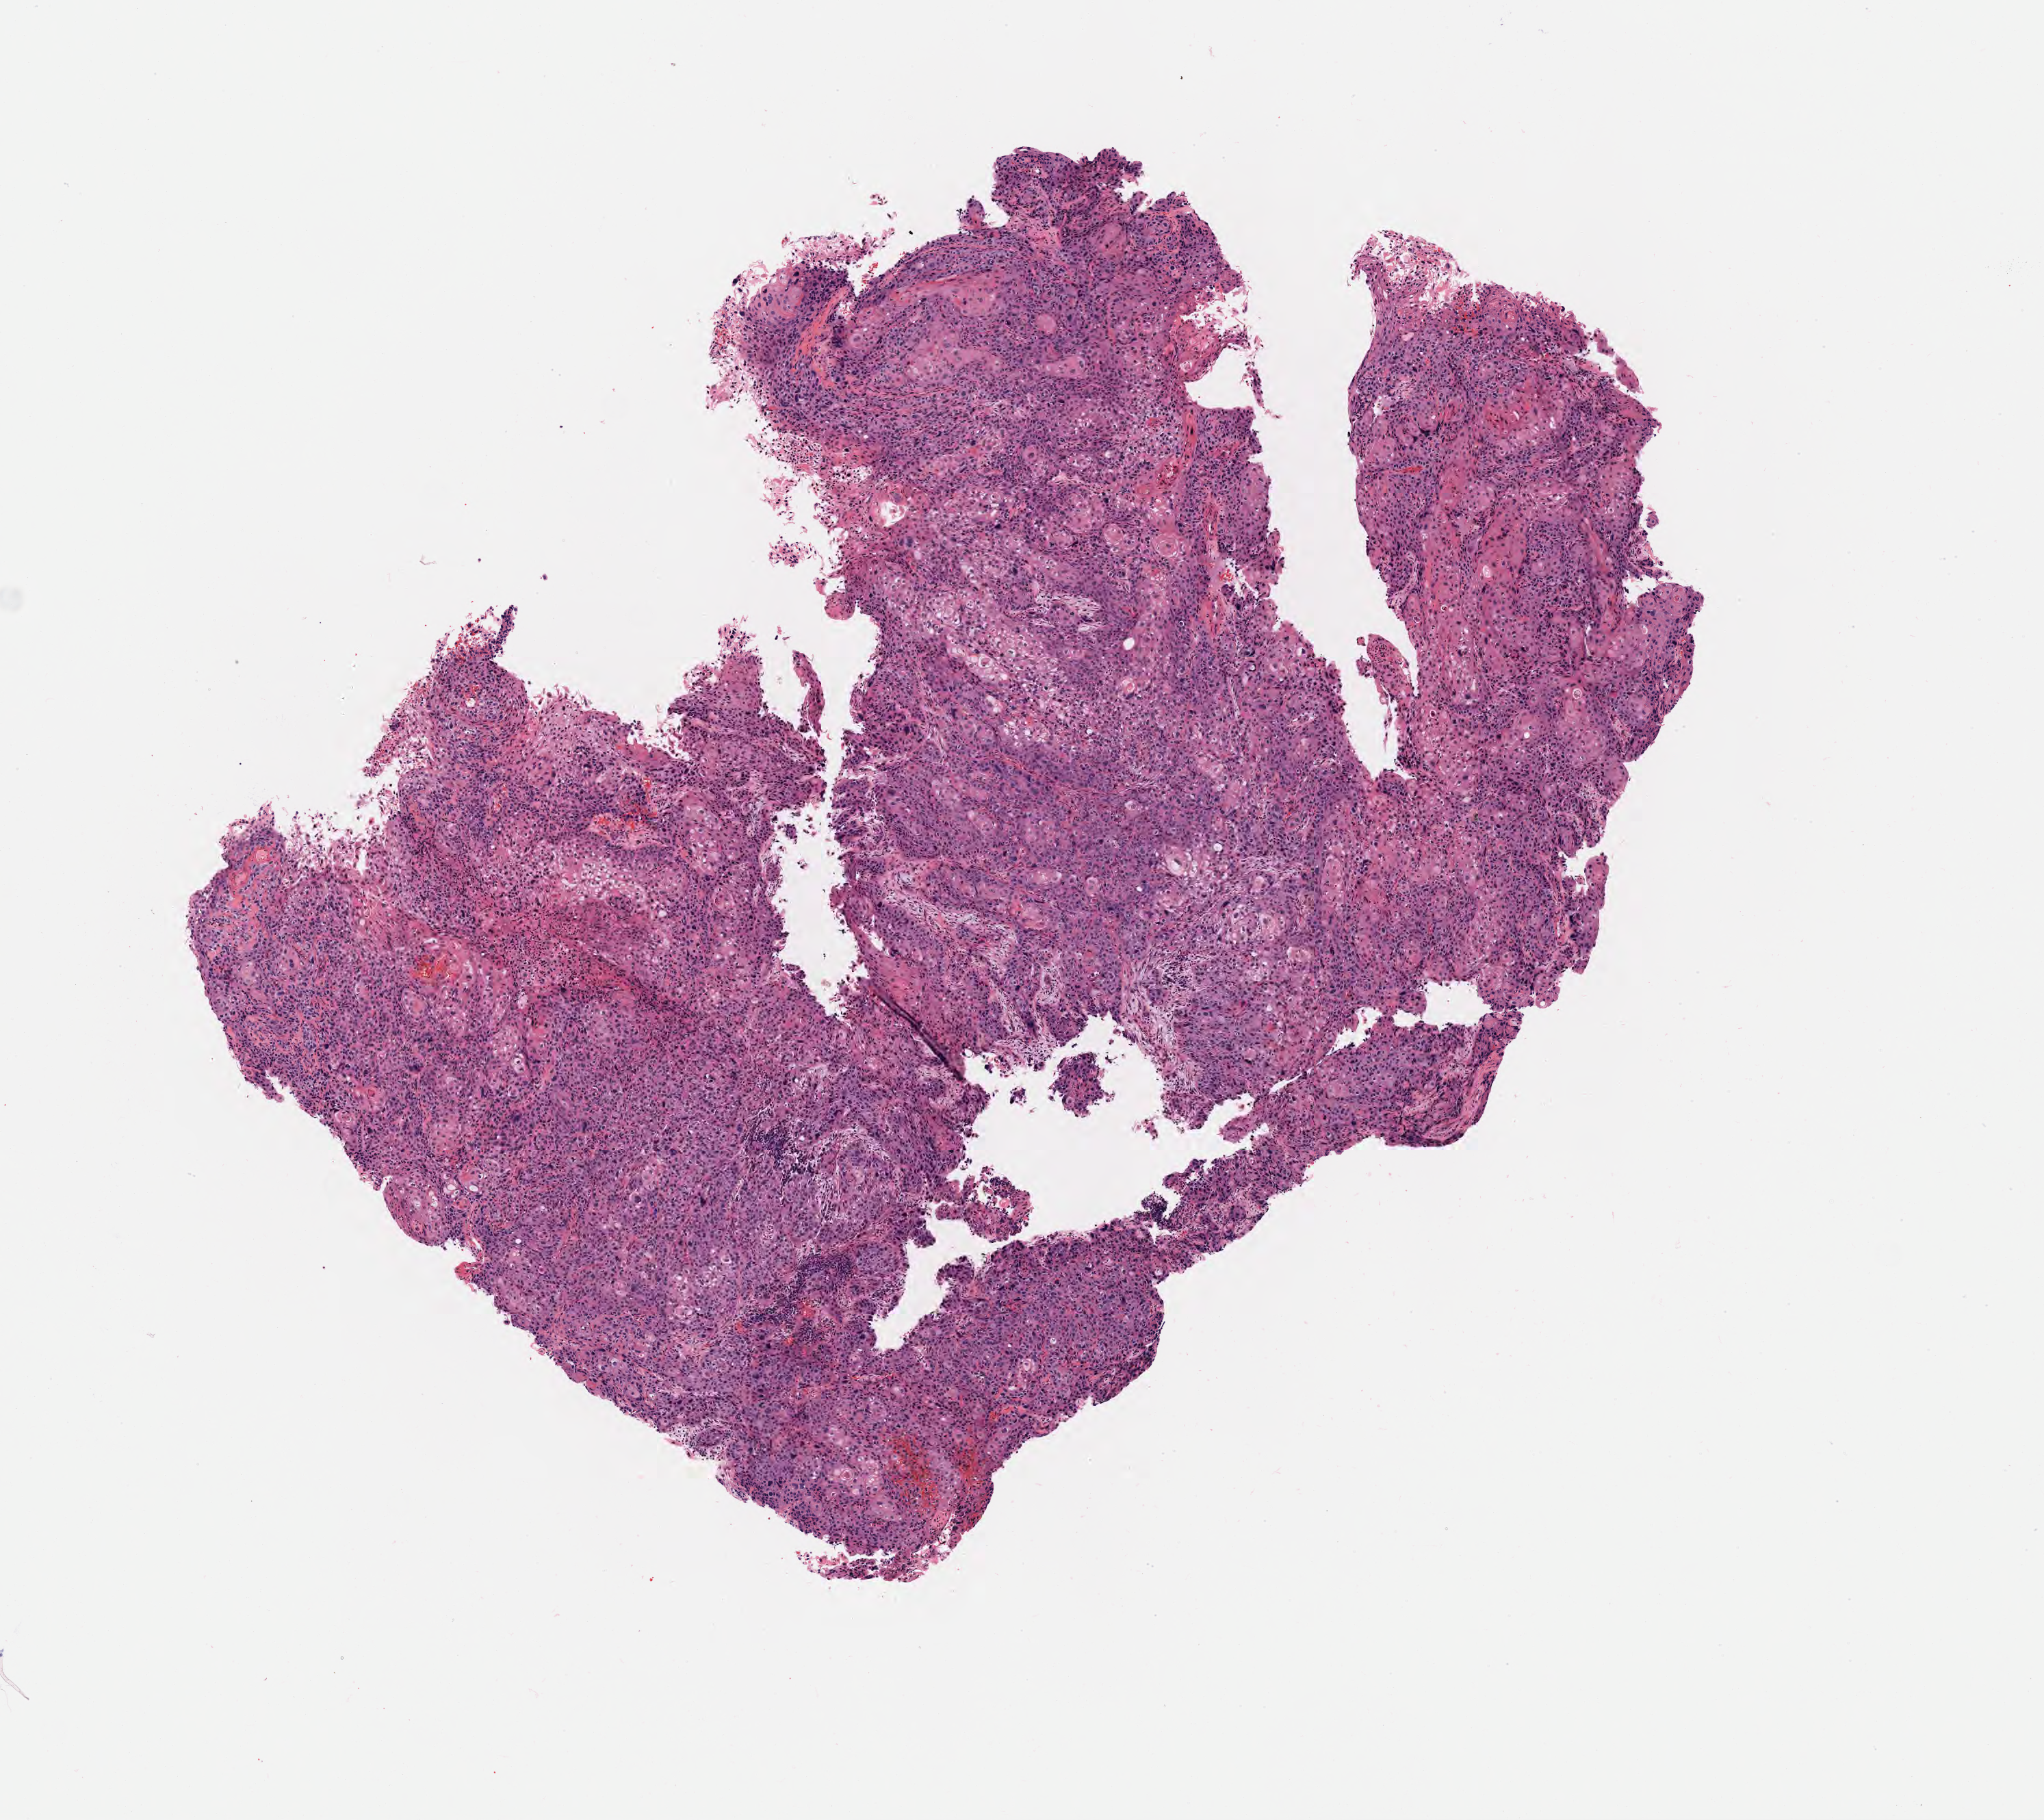
Digitized hematoxylin and eosin (H&E)-stained section, shown as a low-resolution overview of the whole scanned area (about 6.0 x 5.4 mm), specimen: tumor tissue, site: cervix. Female patient, 48 years old.
• diagnosis: Squamous cell carcinoma, keratinizing, NOS